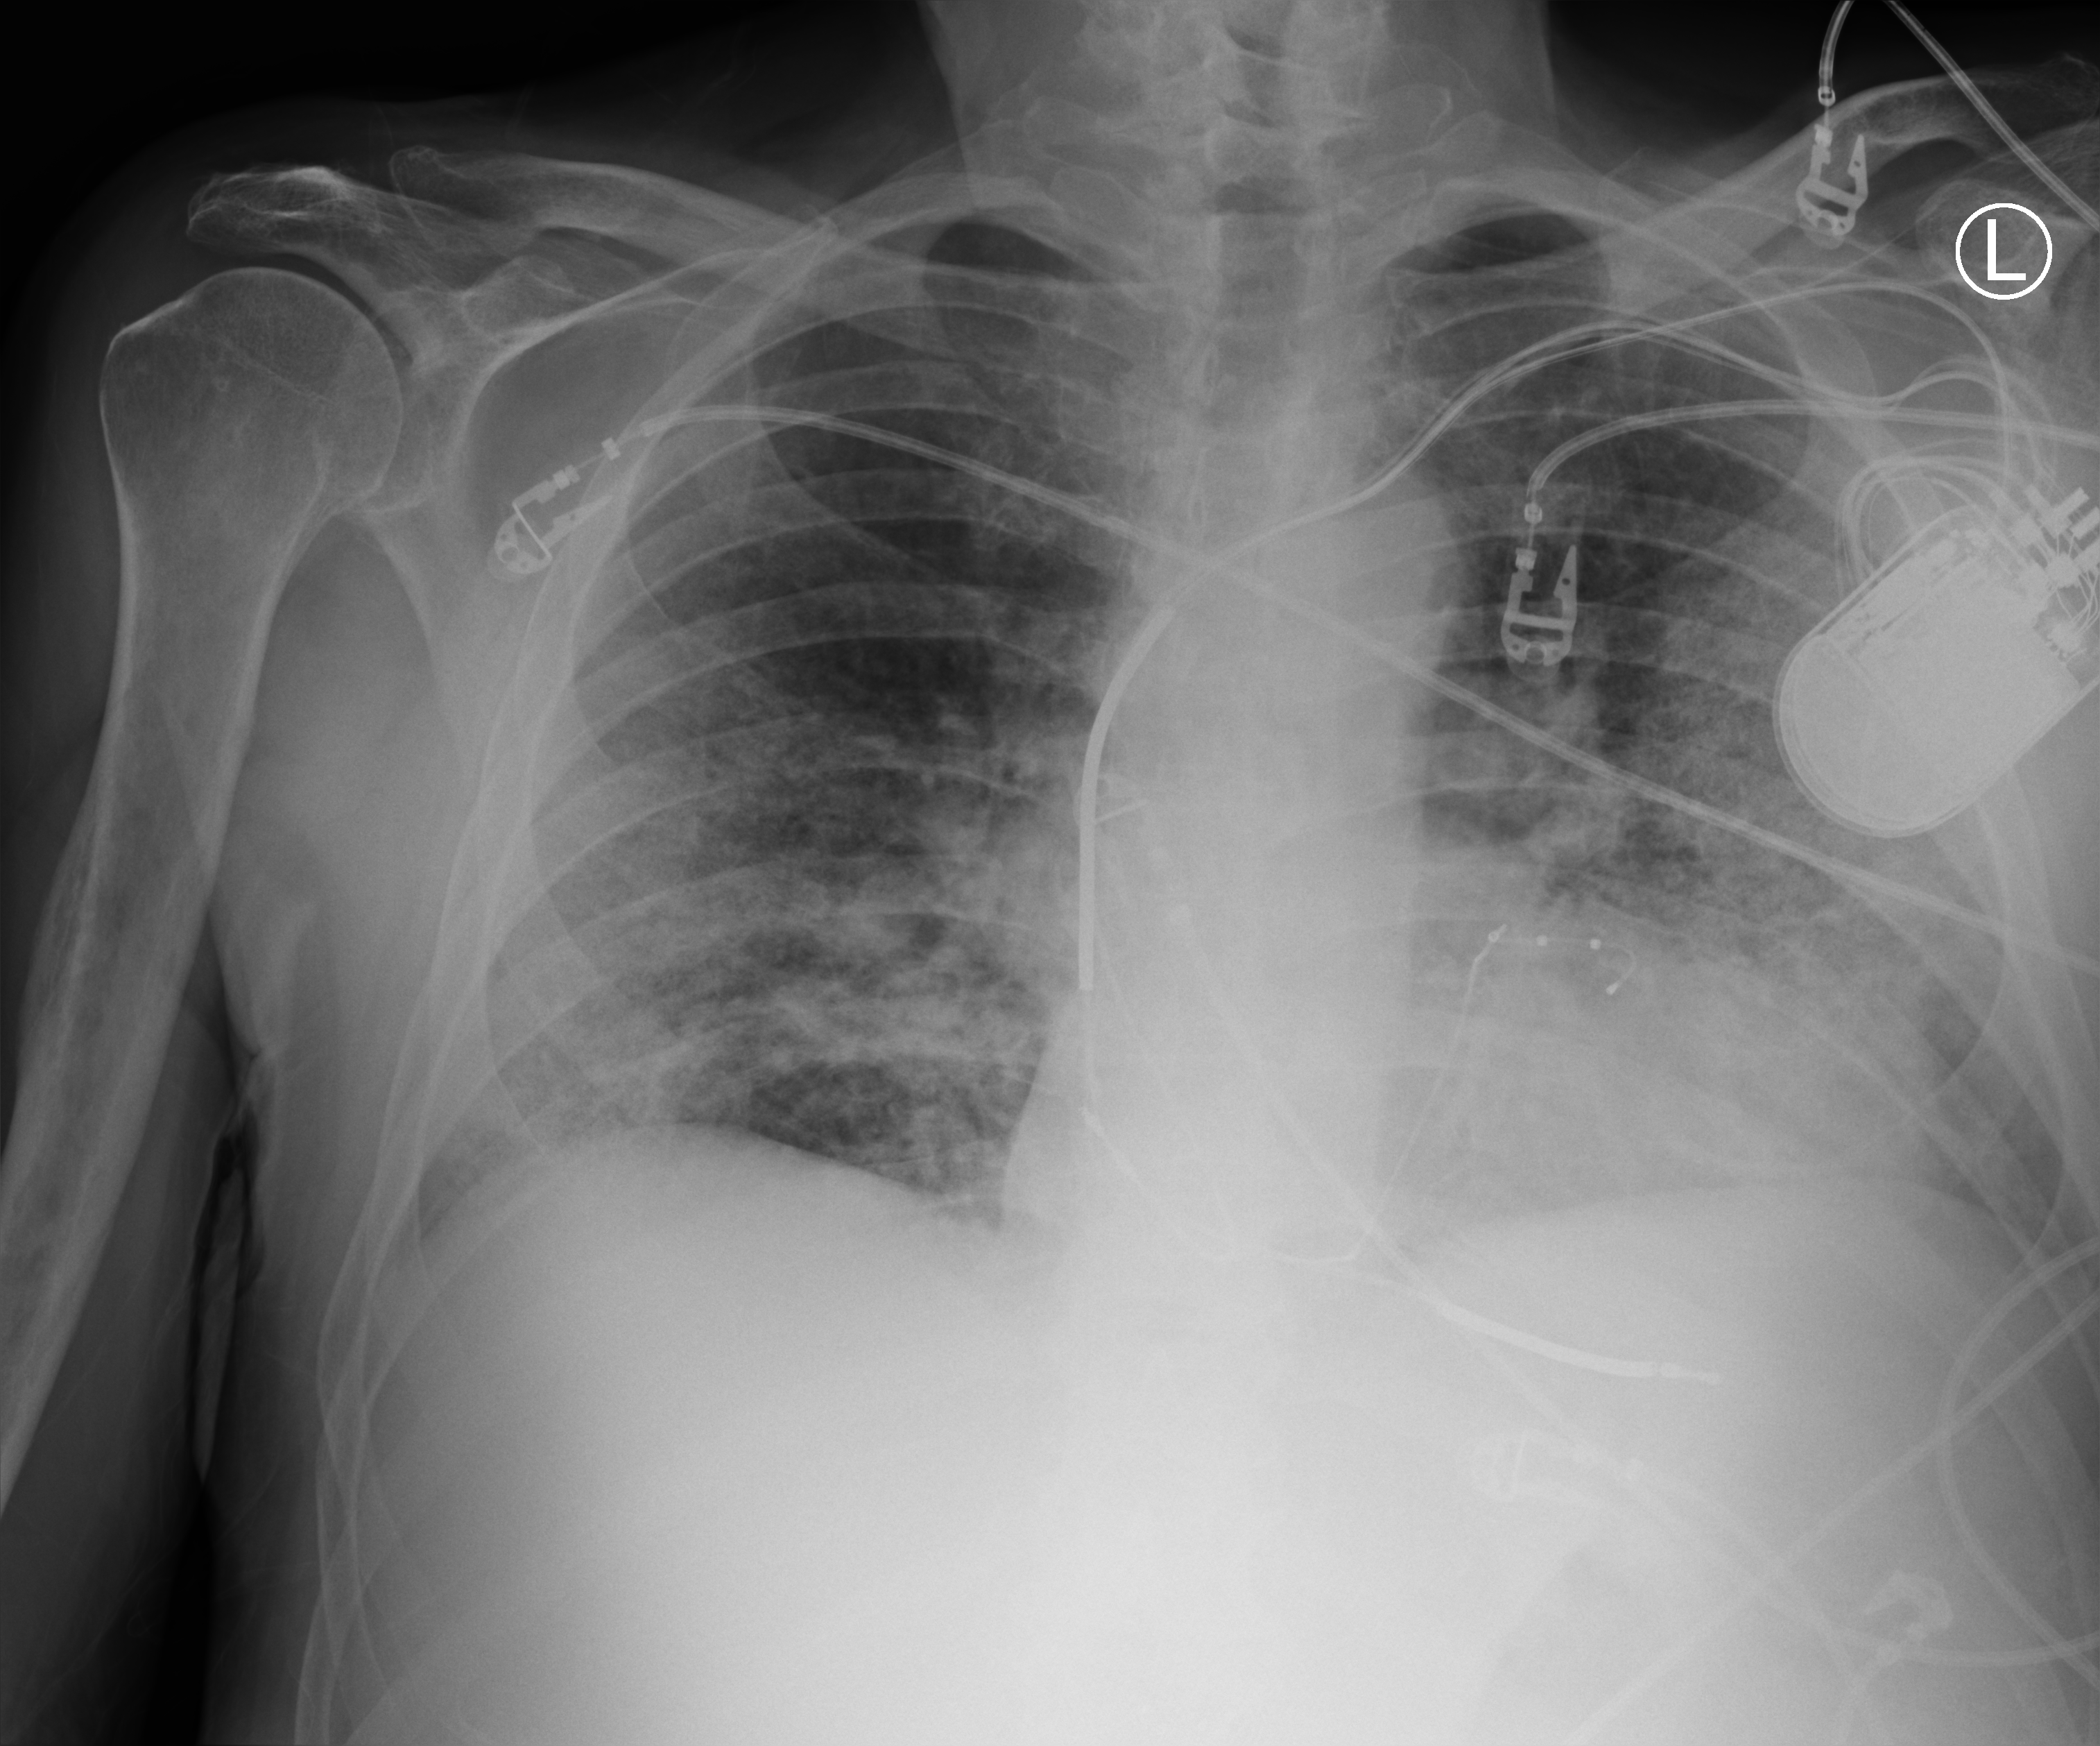
Bedside chest radiograph (computed radiography), anteroposterior (AP) projection. Male patient hospitalised with COVID-19, age 60–74 years.
From the hospital-stay record, not from the radiograph (when in the stay this image was taken is not recorded): admitted to intensive care during this hospital stay: yes; mechanically ventilated during this hospital stay: yes; other chronic lung disease (admission record): no.